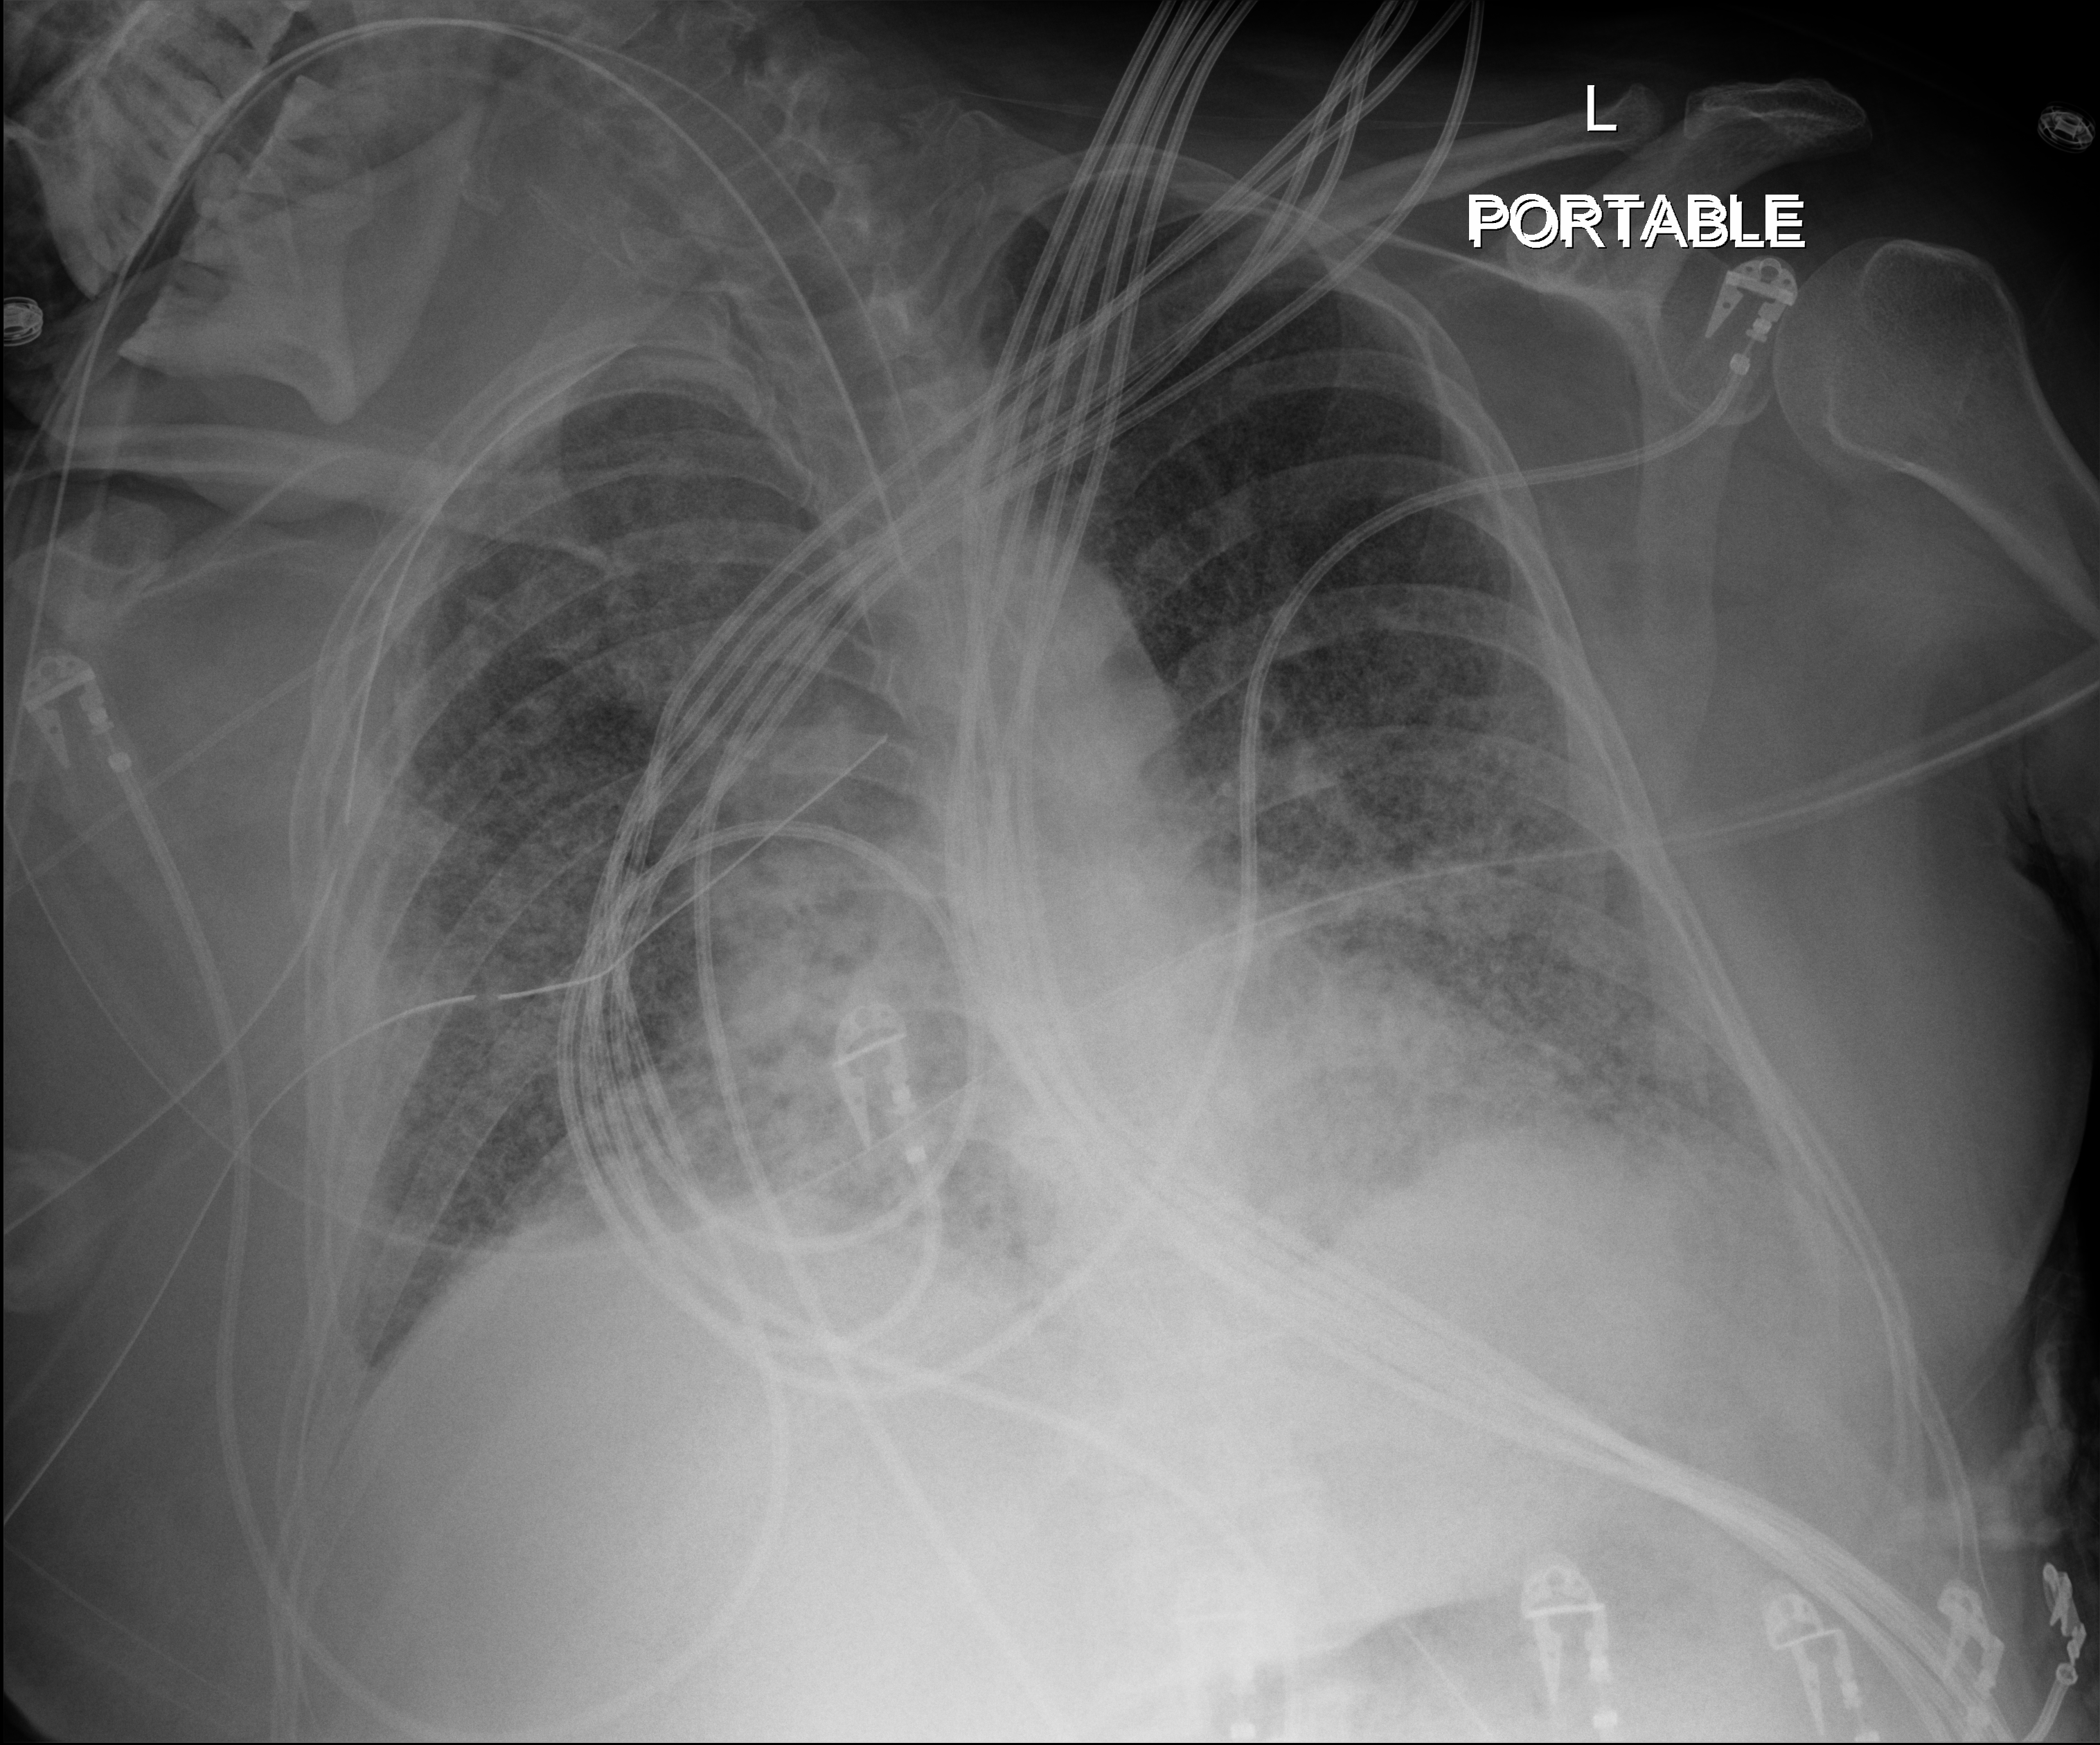
Chest radiograph (digital radiography), anteroposterior (AP) projection. Adult patient hospitalised with COVID-19, age 18–59 years.
From the hospital-stay record, not from the radiograph (when in the stay this image was taken is not recorded): other chronic lung disease (admission record): no.